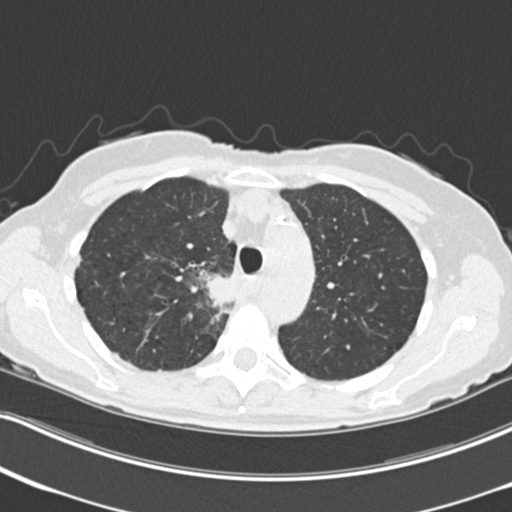
Low-dose screening chest CT, axial slice; third screening round (two years after baseline); lung window (W 1500 / L -600 HU). Female participant, aged 68 years at enrolment.
Expert reader's lesion annotation, bounding box <196,267,249,323> (left, top, right, bottom; pixels). Screening reader's record for this exam (one nodule recorded; not confirmed to be the boxed lesion): non-calcified nodule or mass ≥4 mm, right upper lobe, 31 × 29 mm, poorly defined margins, soft tissue attenuation, pre-existing on the prior screen: no. Official screen result: positive, other. Participant outcome: lung cancer diagnosed 79 days after this screen — squamous cell carcinoma, NOS, right upper lobe, mediastinum, poorly differentiated (G3), stage IIIB (AJCC 6th edition), 43 mm at pathology.